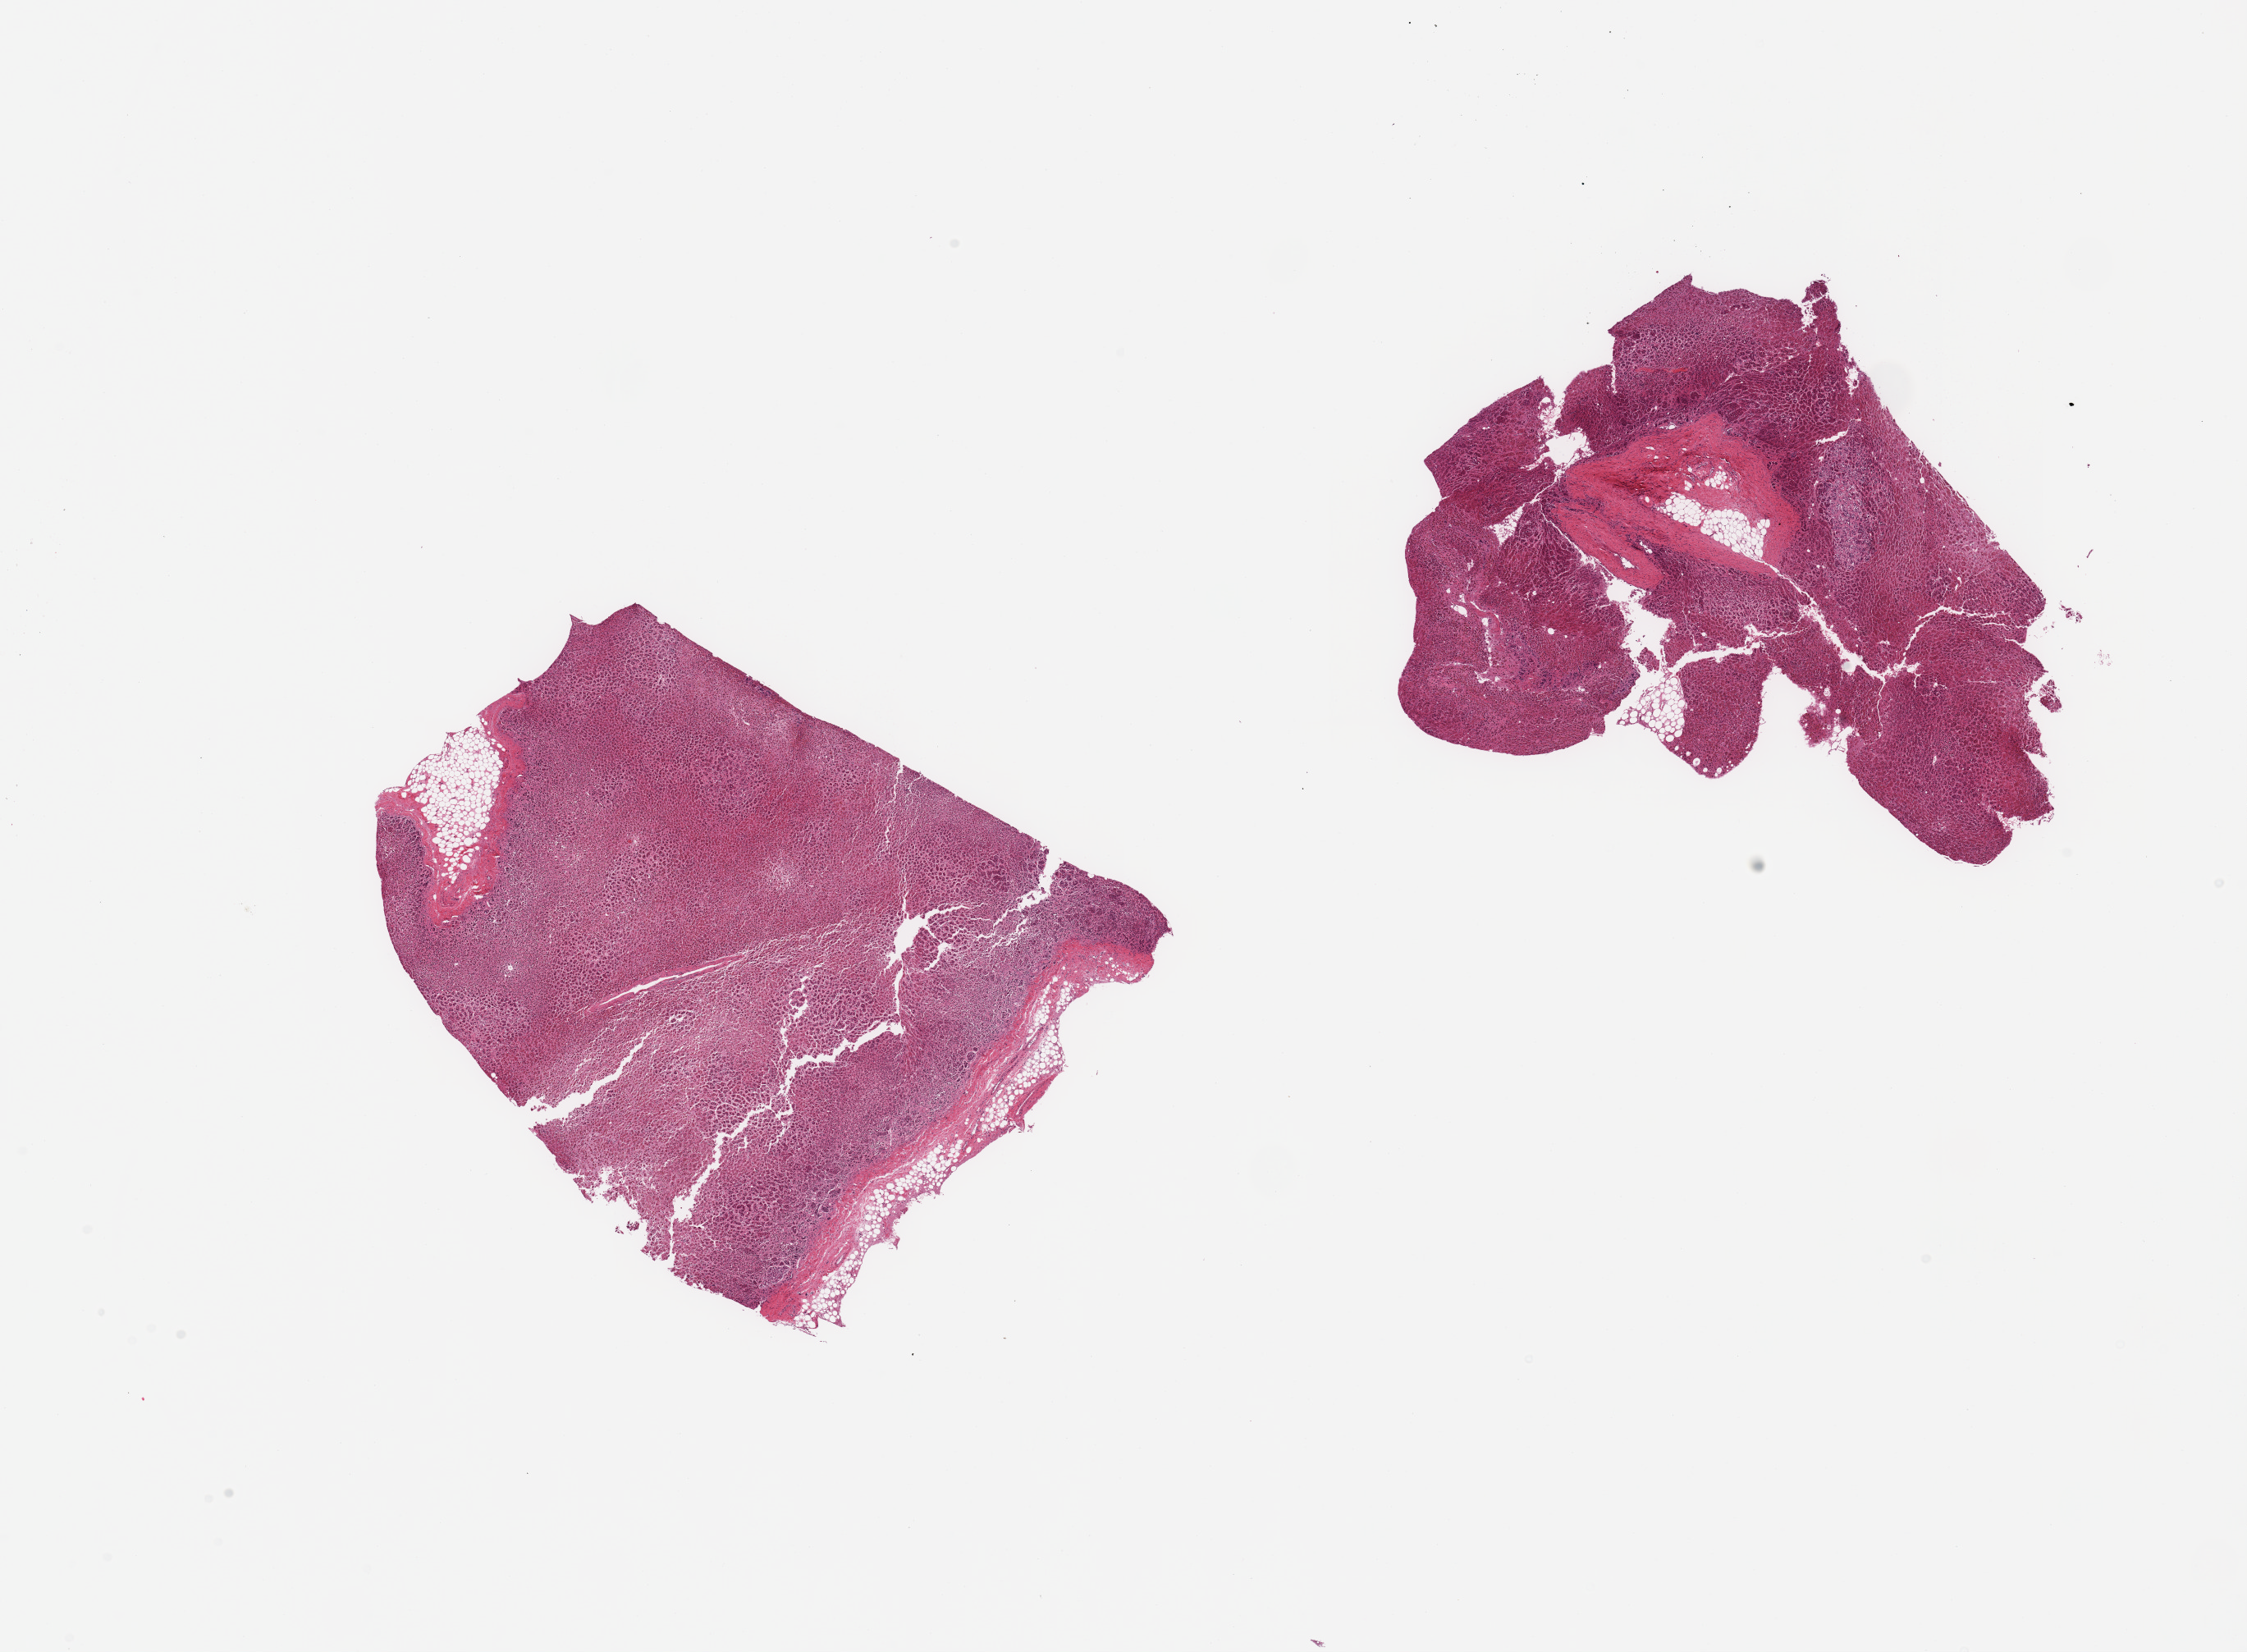
Hematoxylin and eosin (H&E) whole-slide image, brightfield — whole scanned area (about 21.7 x 15.9 mm) shown as a low-resolution overview; PAXgene-fixed, paraffin-embedded tissue; section of adrenal gland (target tissue); donor tissue sample.
Pathologist's review note for this sample: 2 pieces, cortex, ~20$ stroma/fat.